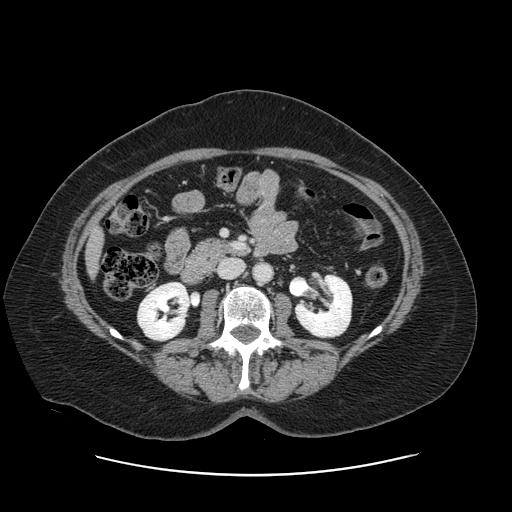
Contrast-enhanced abdominal CT, one axial slice; slice 43 of 161 in the series (ordered by position); 120 kVp; intravenous contrast given; soft-tissue window (W 400 / L 40 HU); 2.5 mm slice thickness; 512 × 512 image matrix. Female patient, age 62 years. Case-level facts recorded for this patient, not image findings: diagnosis: colorectal cancer liver metastases, imaged before liver resection; multiple liver metastases: no; largest metastasis: 2.5 cm; disease in both lobes: no.
Structures marked on this image (expert manual segmentation):
- liver: box from (x=88, y=234) to (x=102, y=271) px